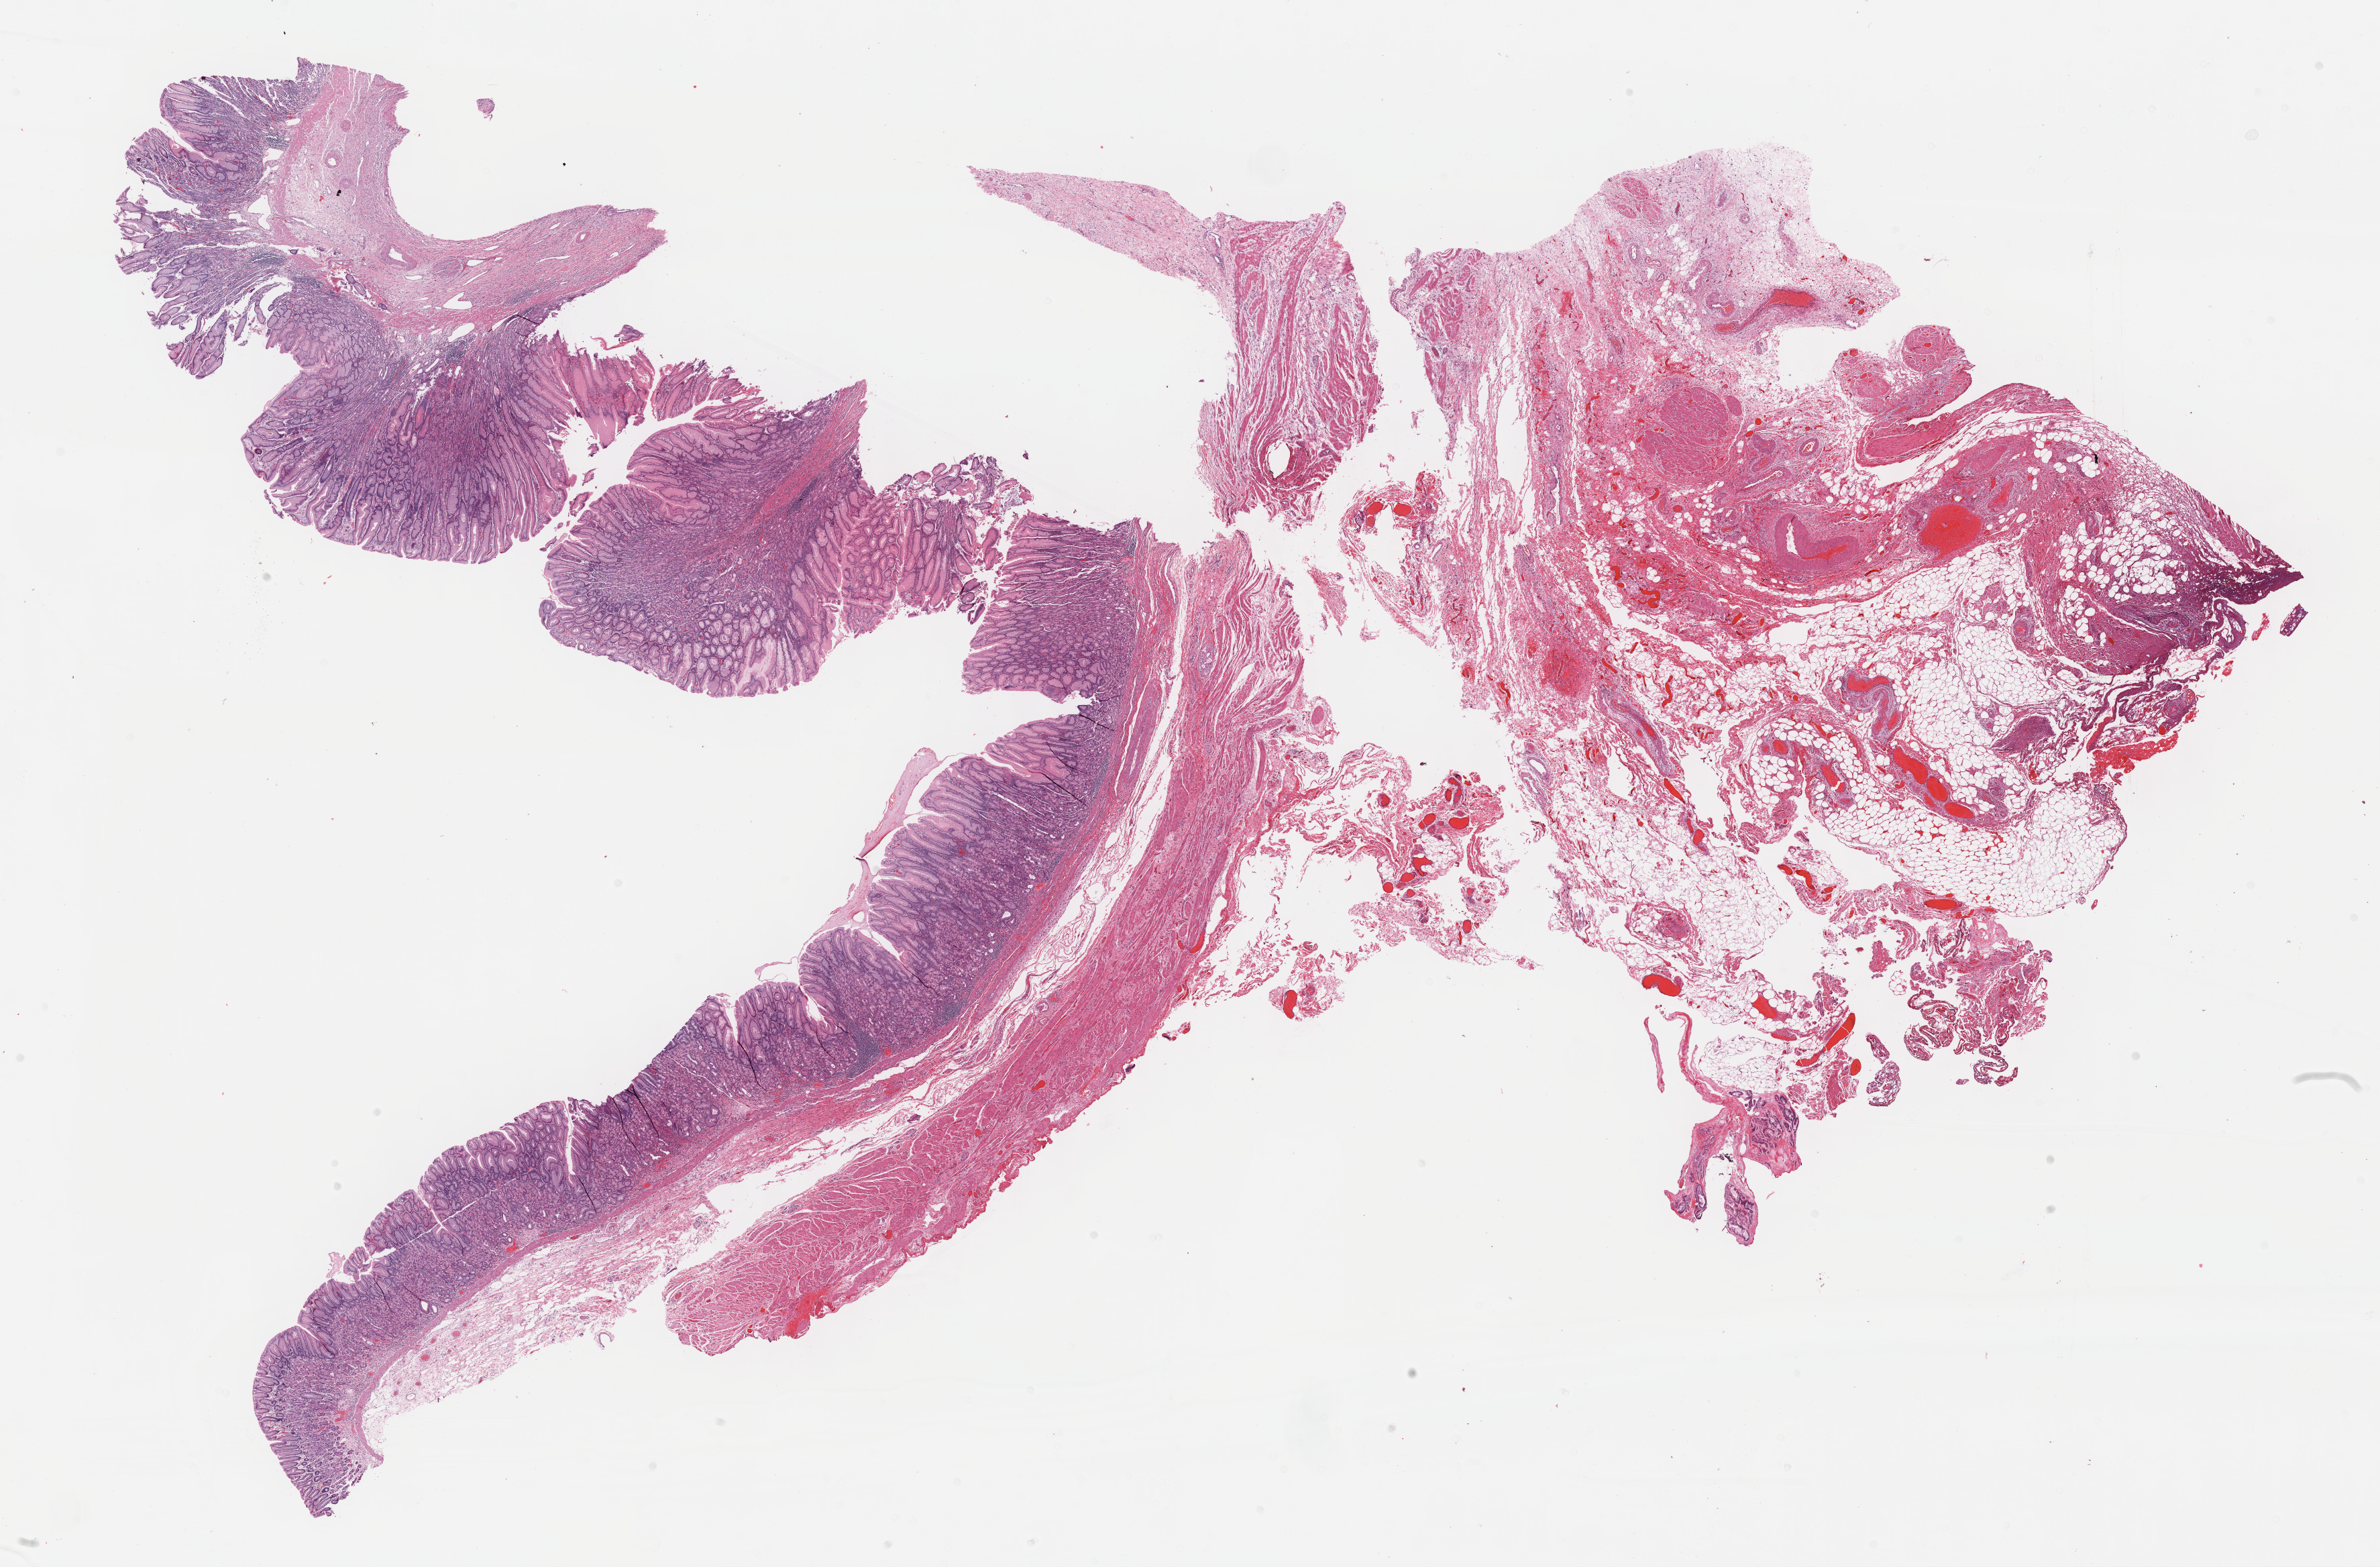
H&E-stained whole-slide image, shown as a low-resolution overview of the whole scanned area (about 28.7 x 18.9 mm, acquisition: 40x scan), formalin-fixed paraffin-embedded (FFPE) diagnostic section, stomach, primary tumour sample. Patient: female, age at initial diagnosis 58 years.
Pathologic diagnosis: Leiomyosarcoma, NOS.